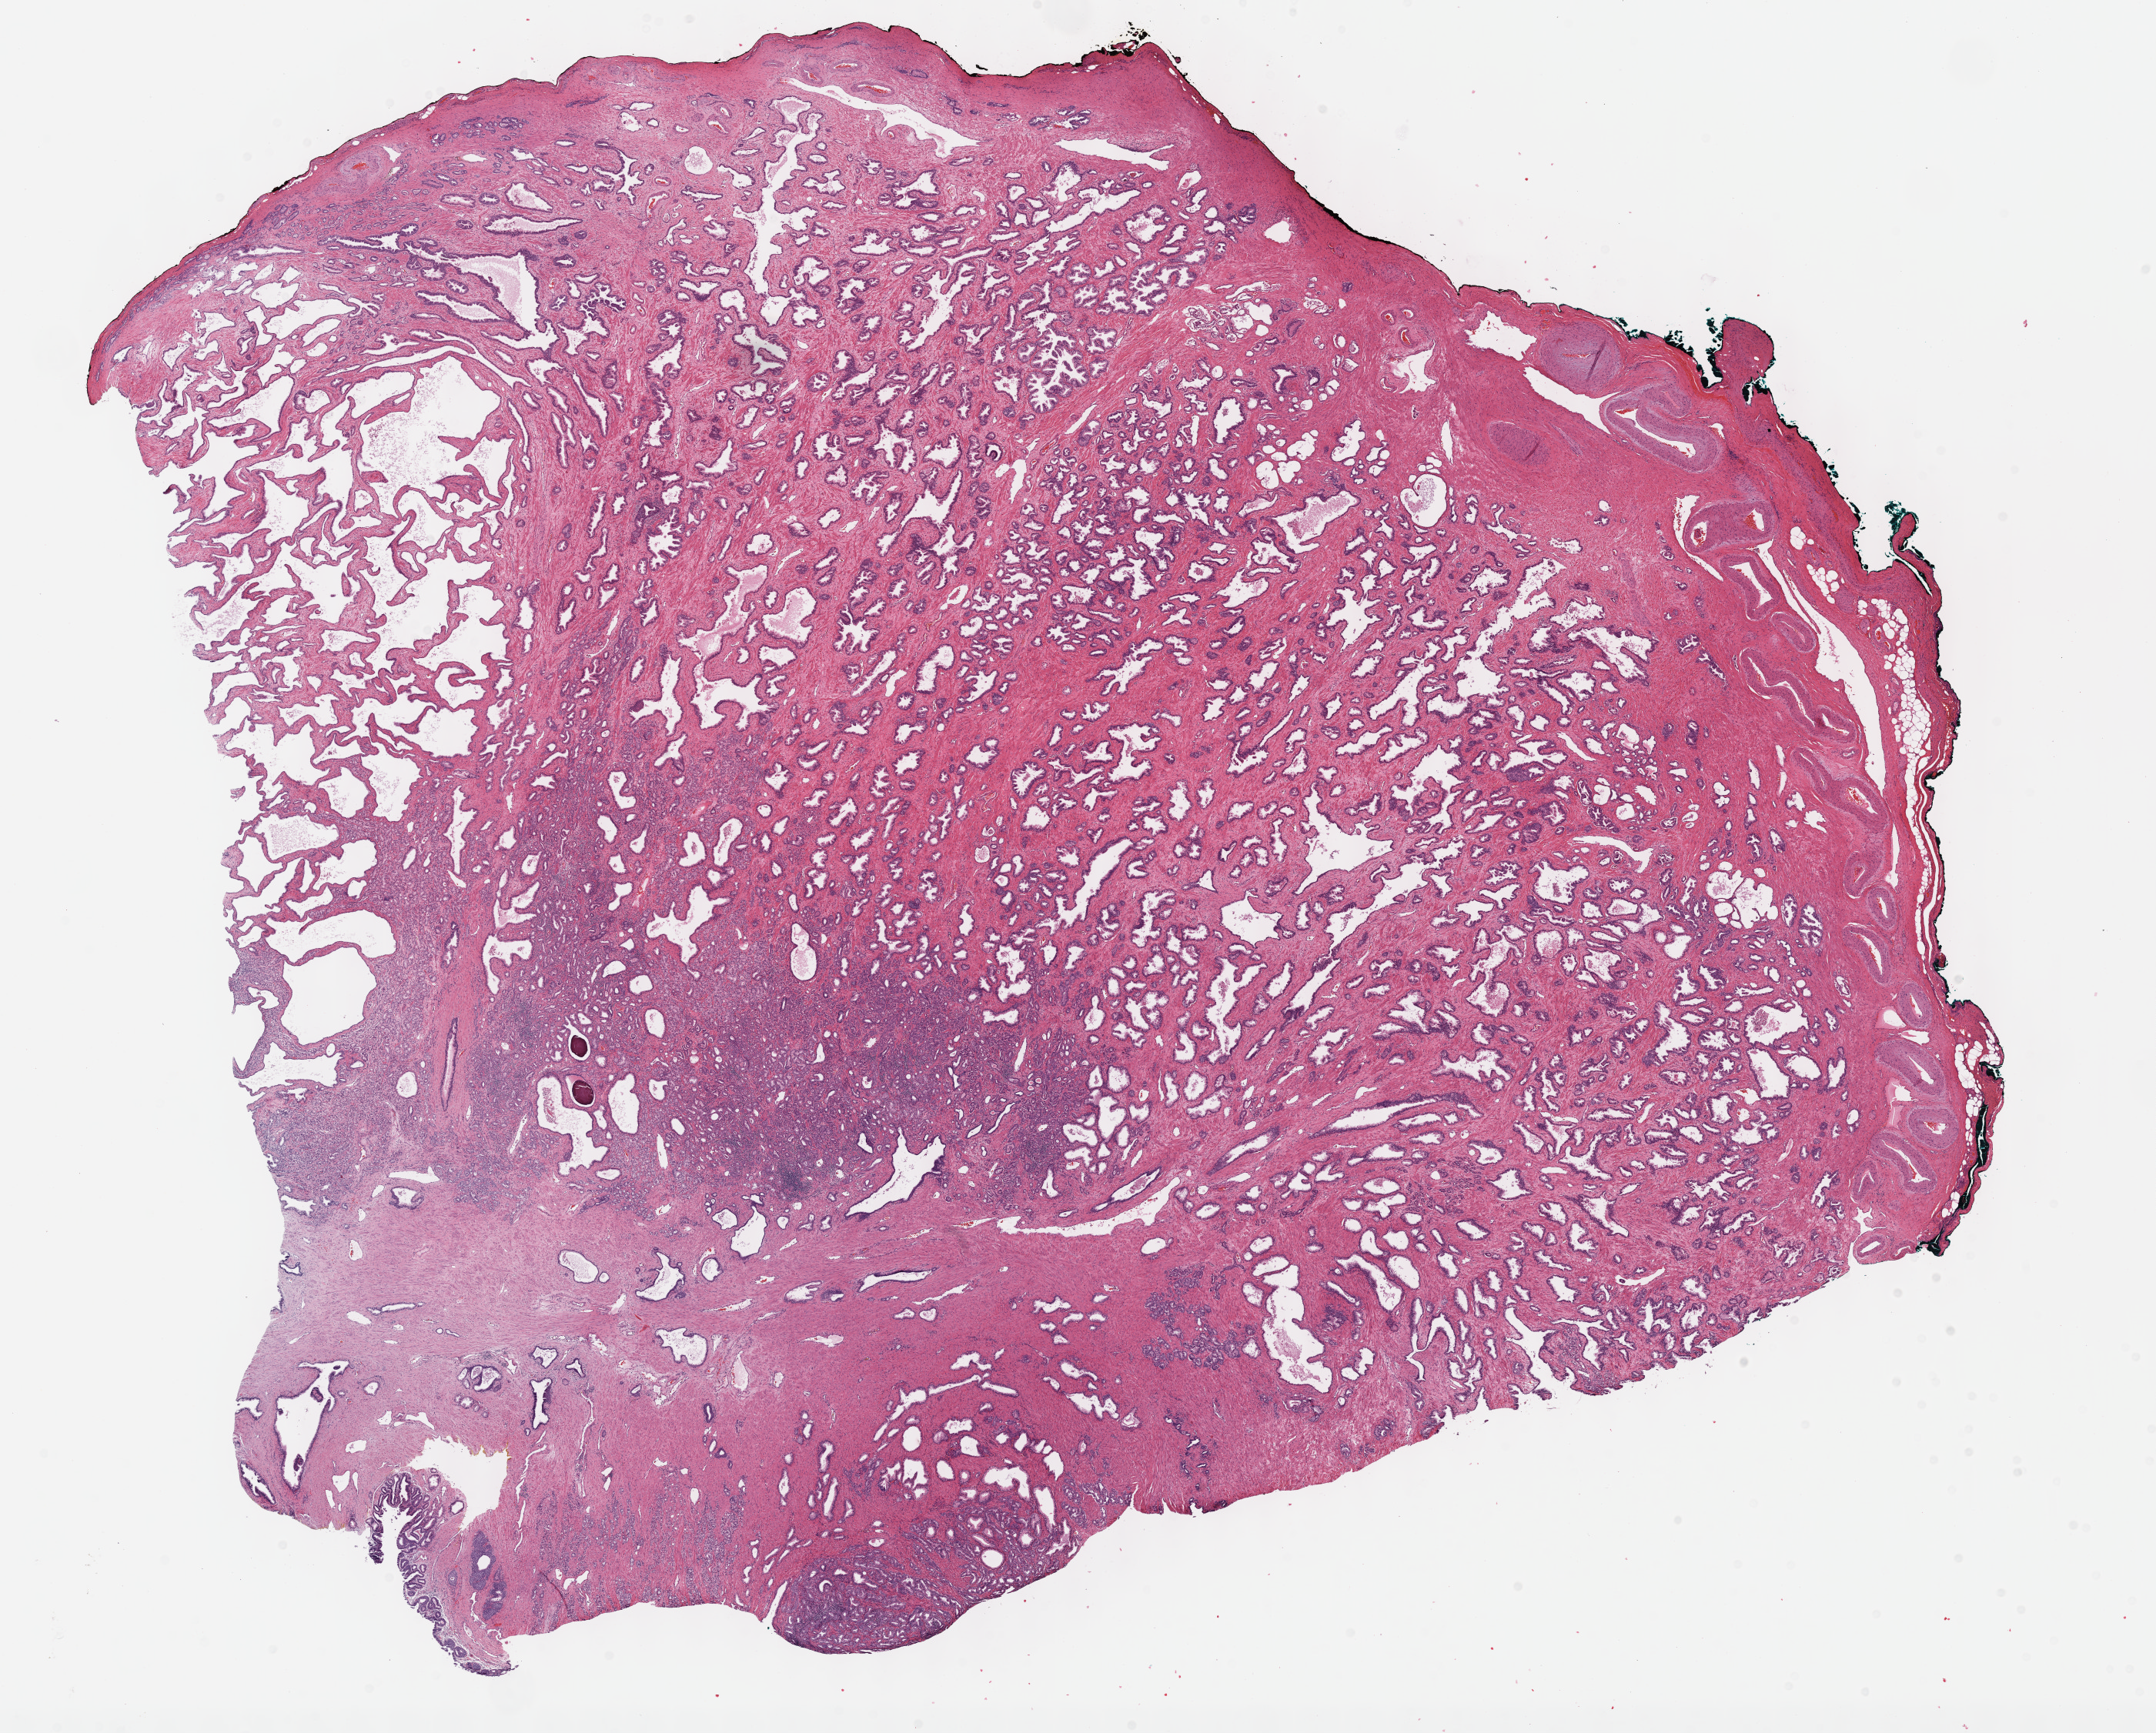
H&E whole-slide image — shown as a low-resolution overview of the whole scanned area (about 22.7 x 18.2 mm); formalin-fixed paraffin-embedded (FFPE) diagnostic section; primary tumour sample from the prostate. Male patient; age at initial diagnosis 53 years. Gleason score: 7 (3+4).
Histologic diagnosis: Acinar cell carcinoma (prostate gland).